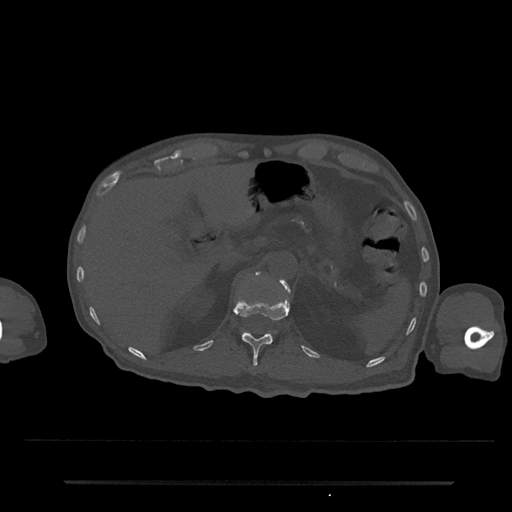
CT including the spine, one axial slice; slice 180 of 797 in the series (ordered by position); reconstruction kernel Br40s/3; bone window (W 1800 / L 400 HU); 512 × 512 image matrix, field of view 427 × 427 mm. Patient: male, 74 years. Case-level facts recorded for this patient, not image findings: primary cancer: prostate.
Annotated regions visible in this slice (semi-automatically segmented with operator editing):
- L1 vertebra: box from (x=240, y=272) to (x=290, y=335) px
- T12 vertebra: (x=234, y=298)–(x=289, y=367)